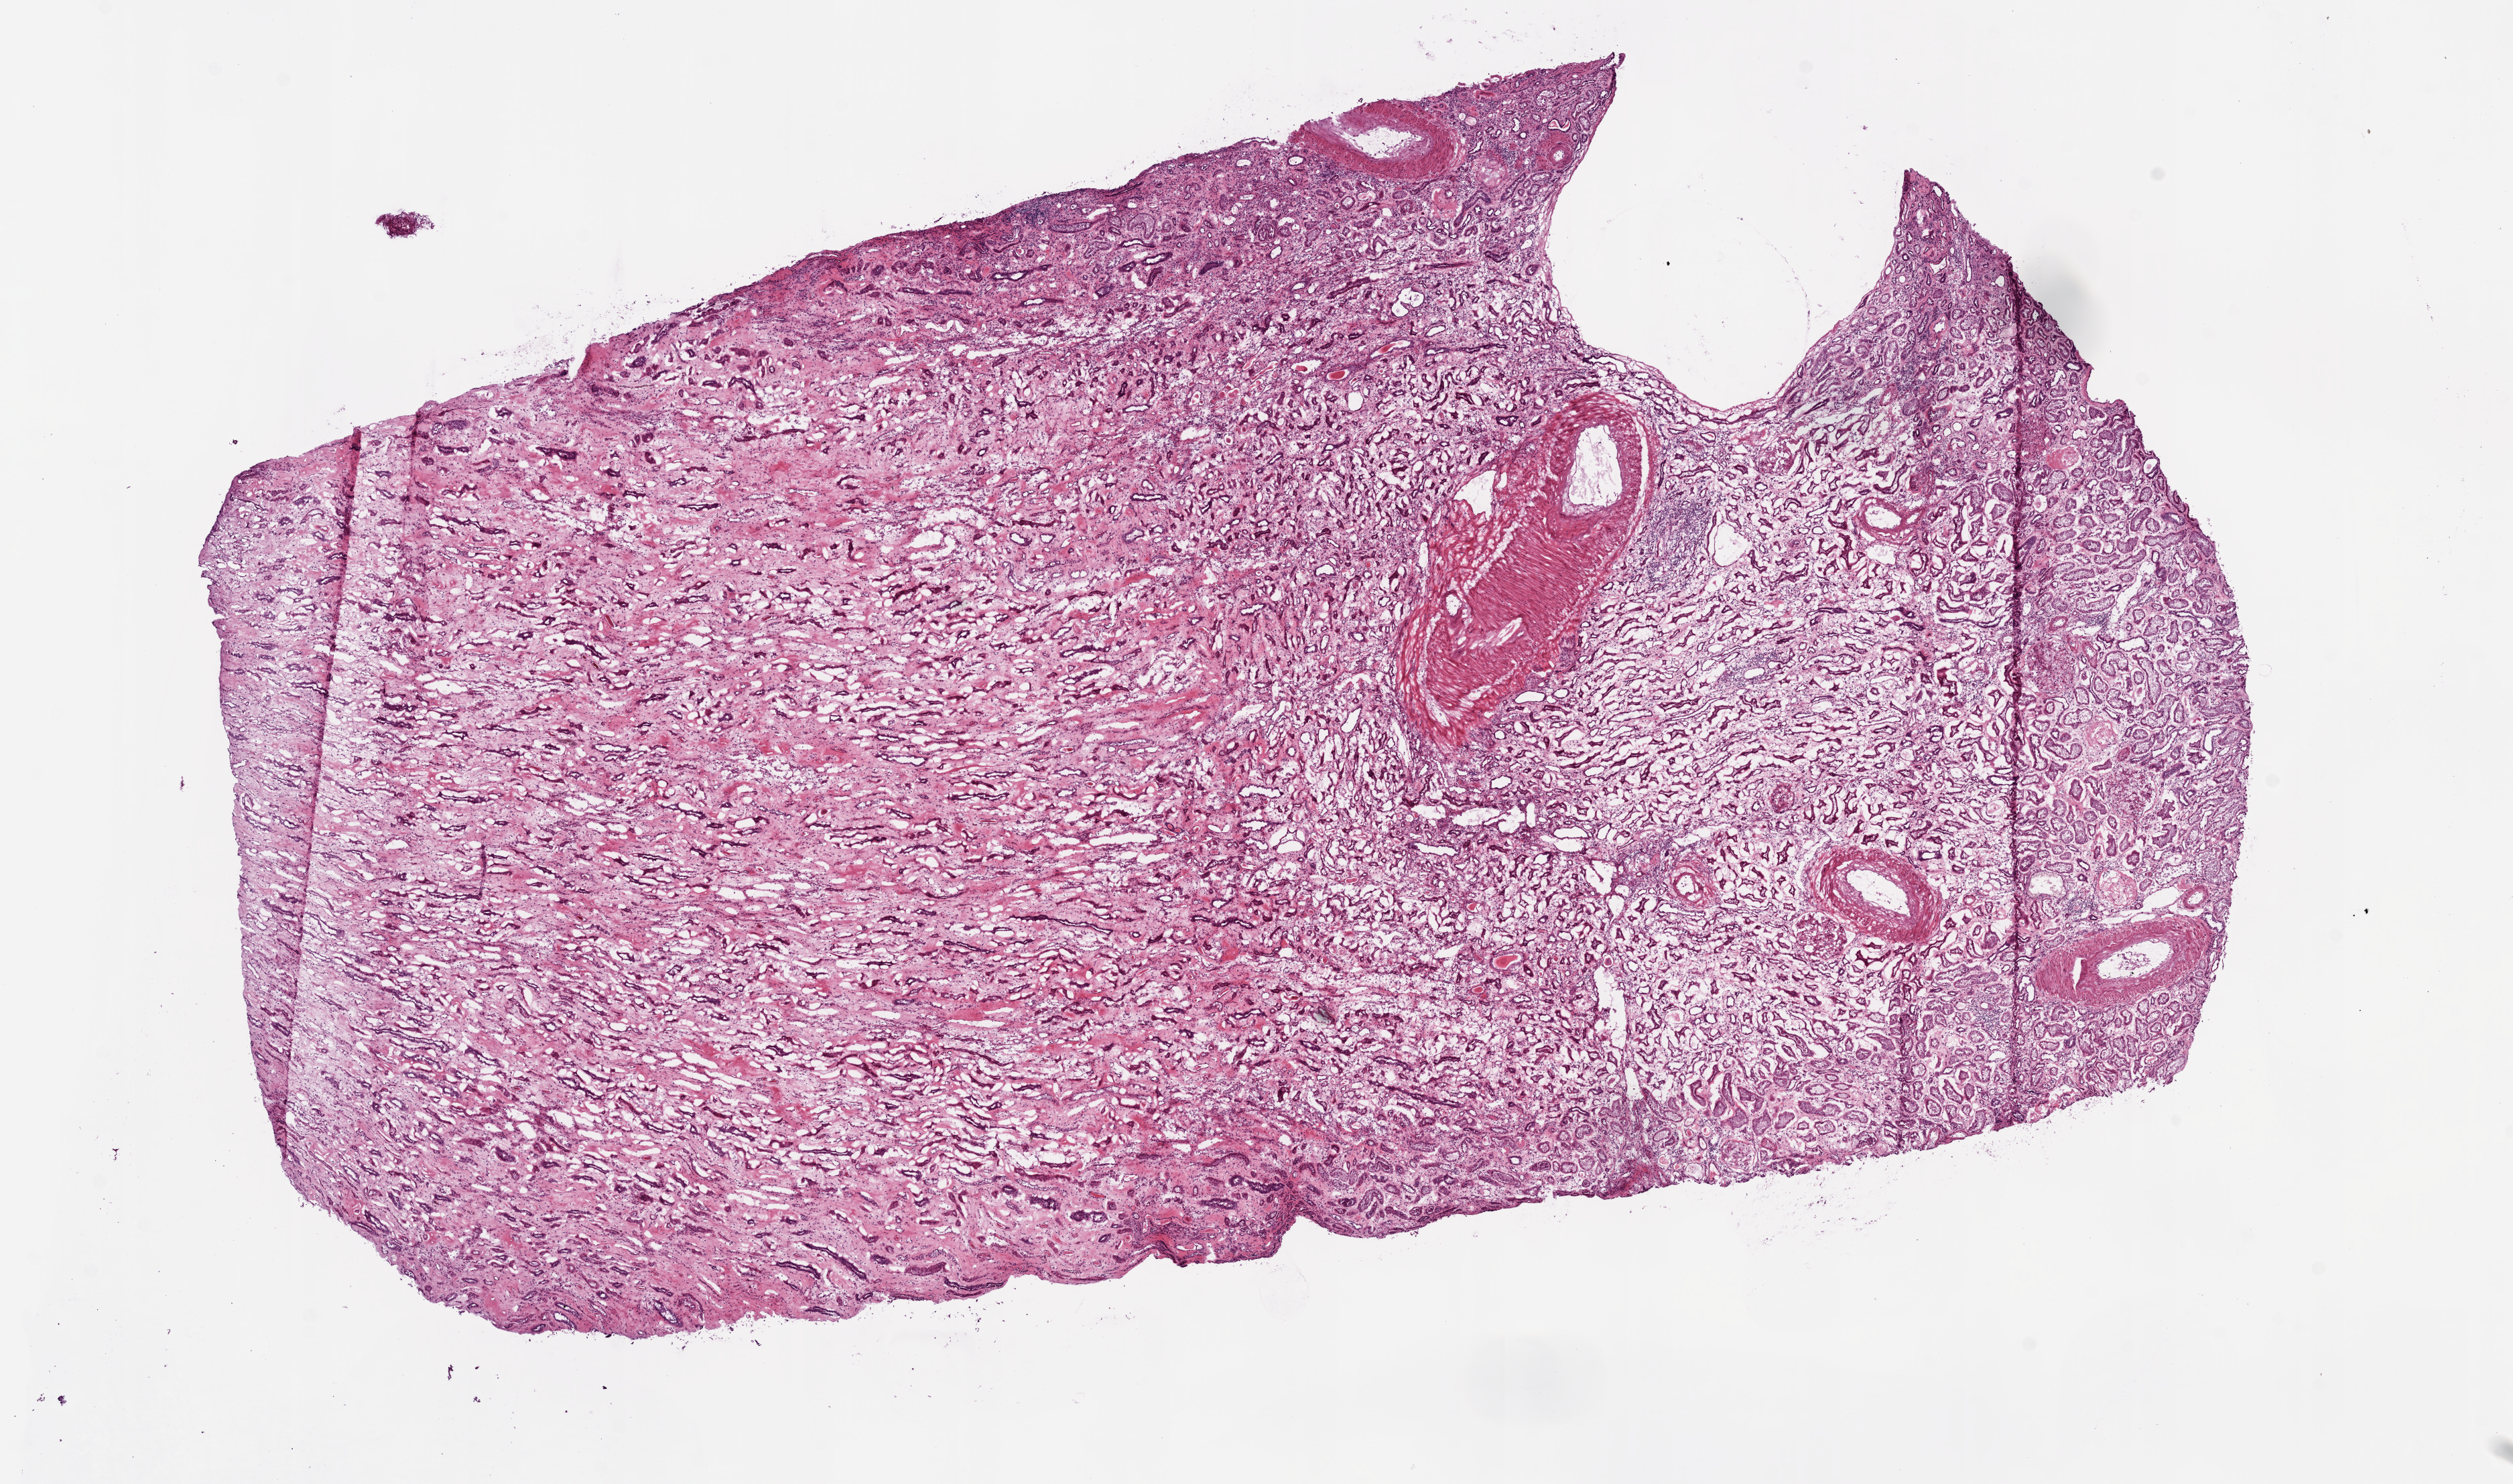
Whole-slide histology image, Hematoxylin and eosin (H&E) stained — low-resolution overview of the scanned area, about 15.0 x 8.9 mm (acquisition: 20x scan); frozen section from the bottom of the tissue portion; sample: solid tissue normal (non-tumour tissue), kidney. Male patient; age at initial diagnosis 70 years.
- this section: solid tissue normal sample (biorepository sample class)
- patient diagnosis: Clear cell adenocarcinoma, NOS